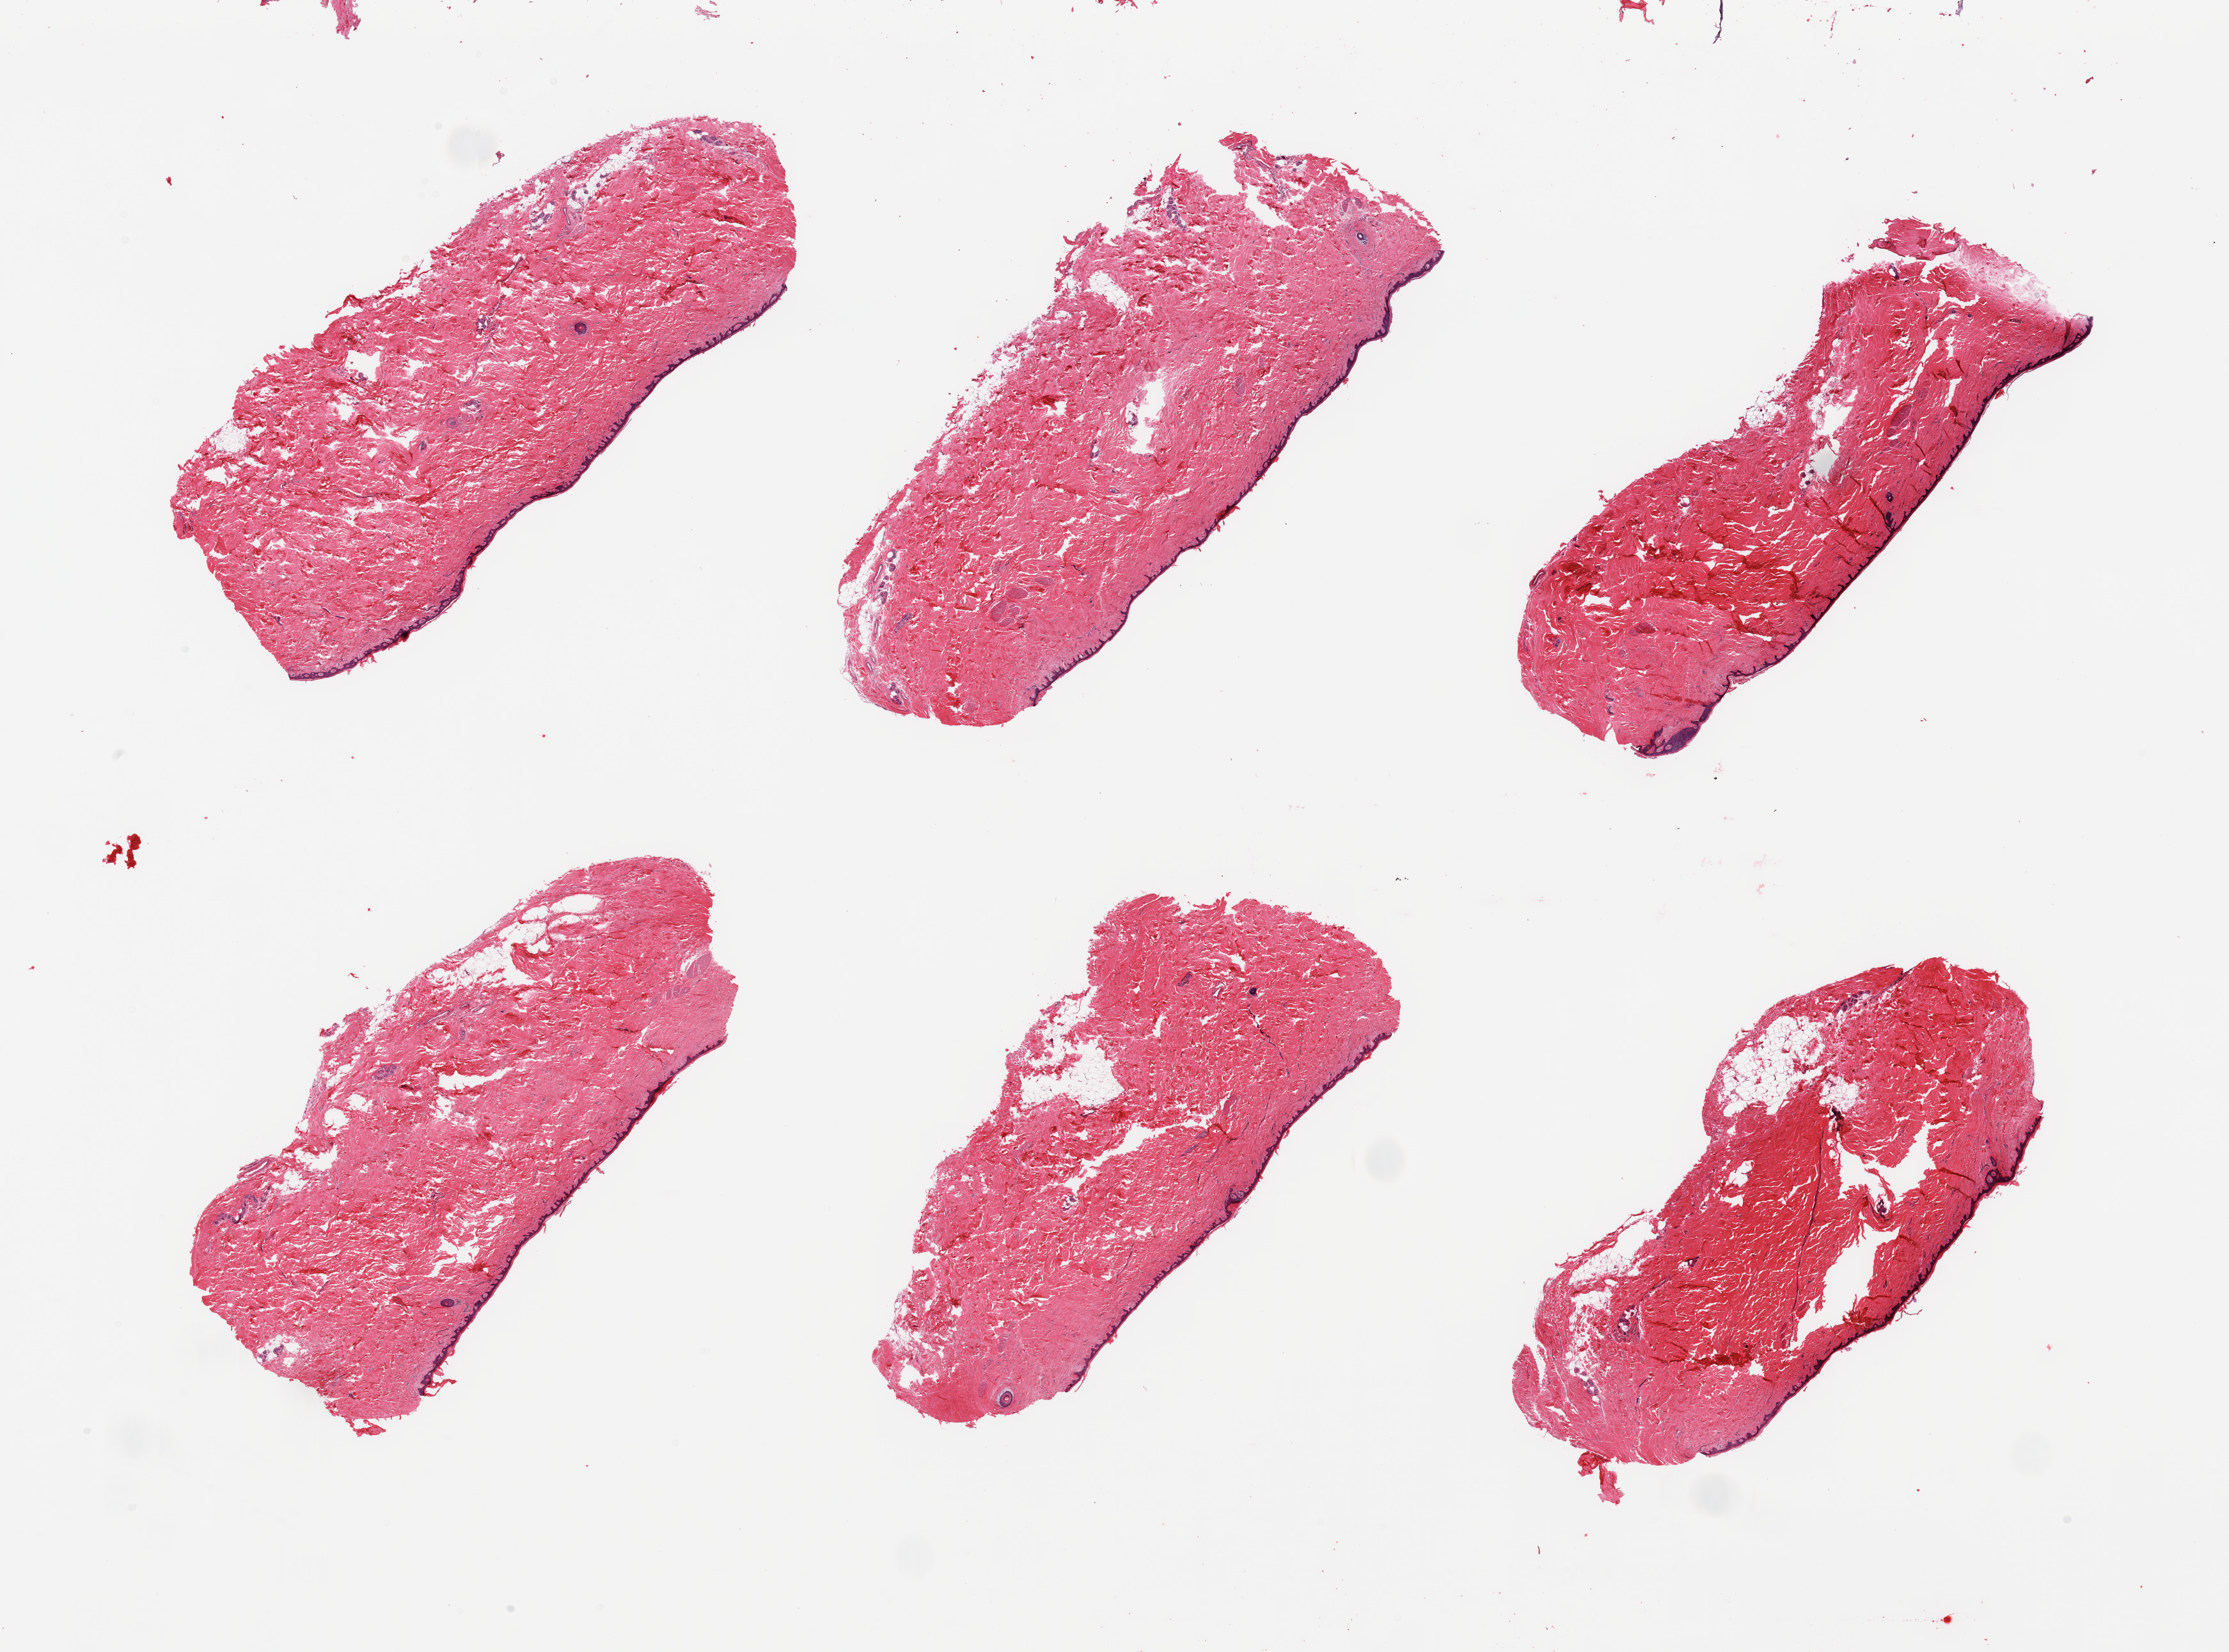
Digitized haematoxylin and eosin-stained section — whole scanned area (about 27.6 x 20.4 mm) shown as a low-resolution overview. PAXgene-fixed, paraffin-embedded tissue. Target tissue: skin of suprapubic region. Tissue donor sample. Donor: female.
Pathologist's review note for this sample: 6 pieces; well trimmed; 5-10% dermal fat.